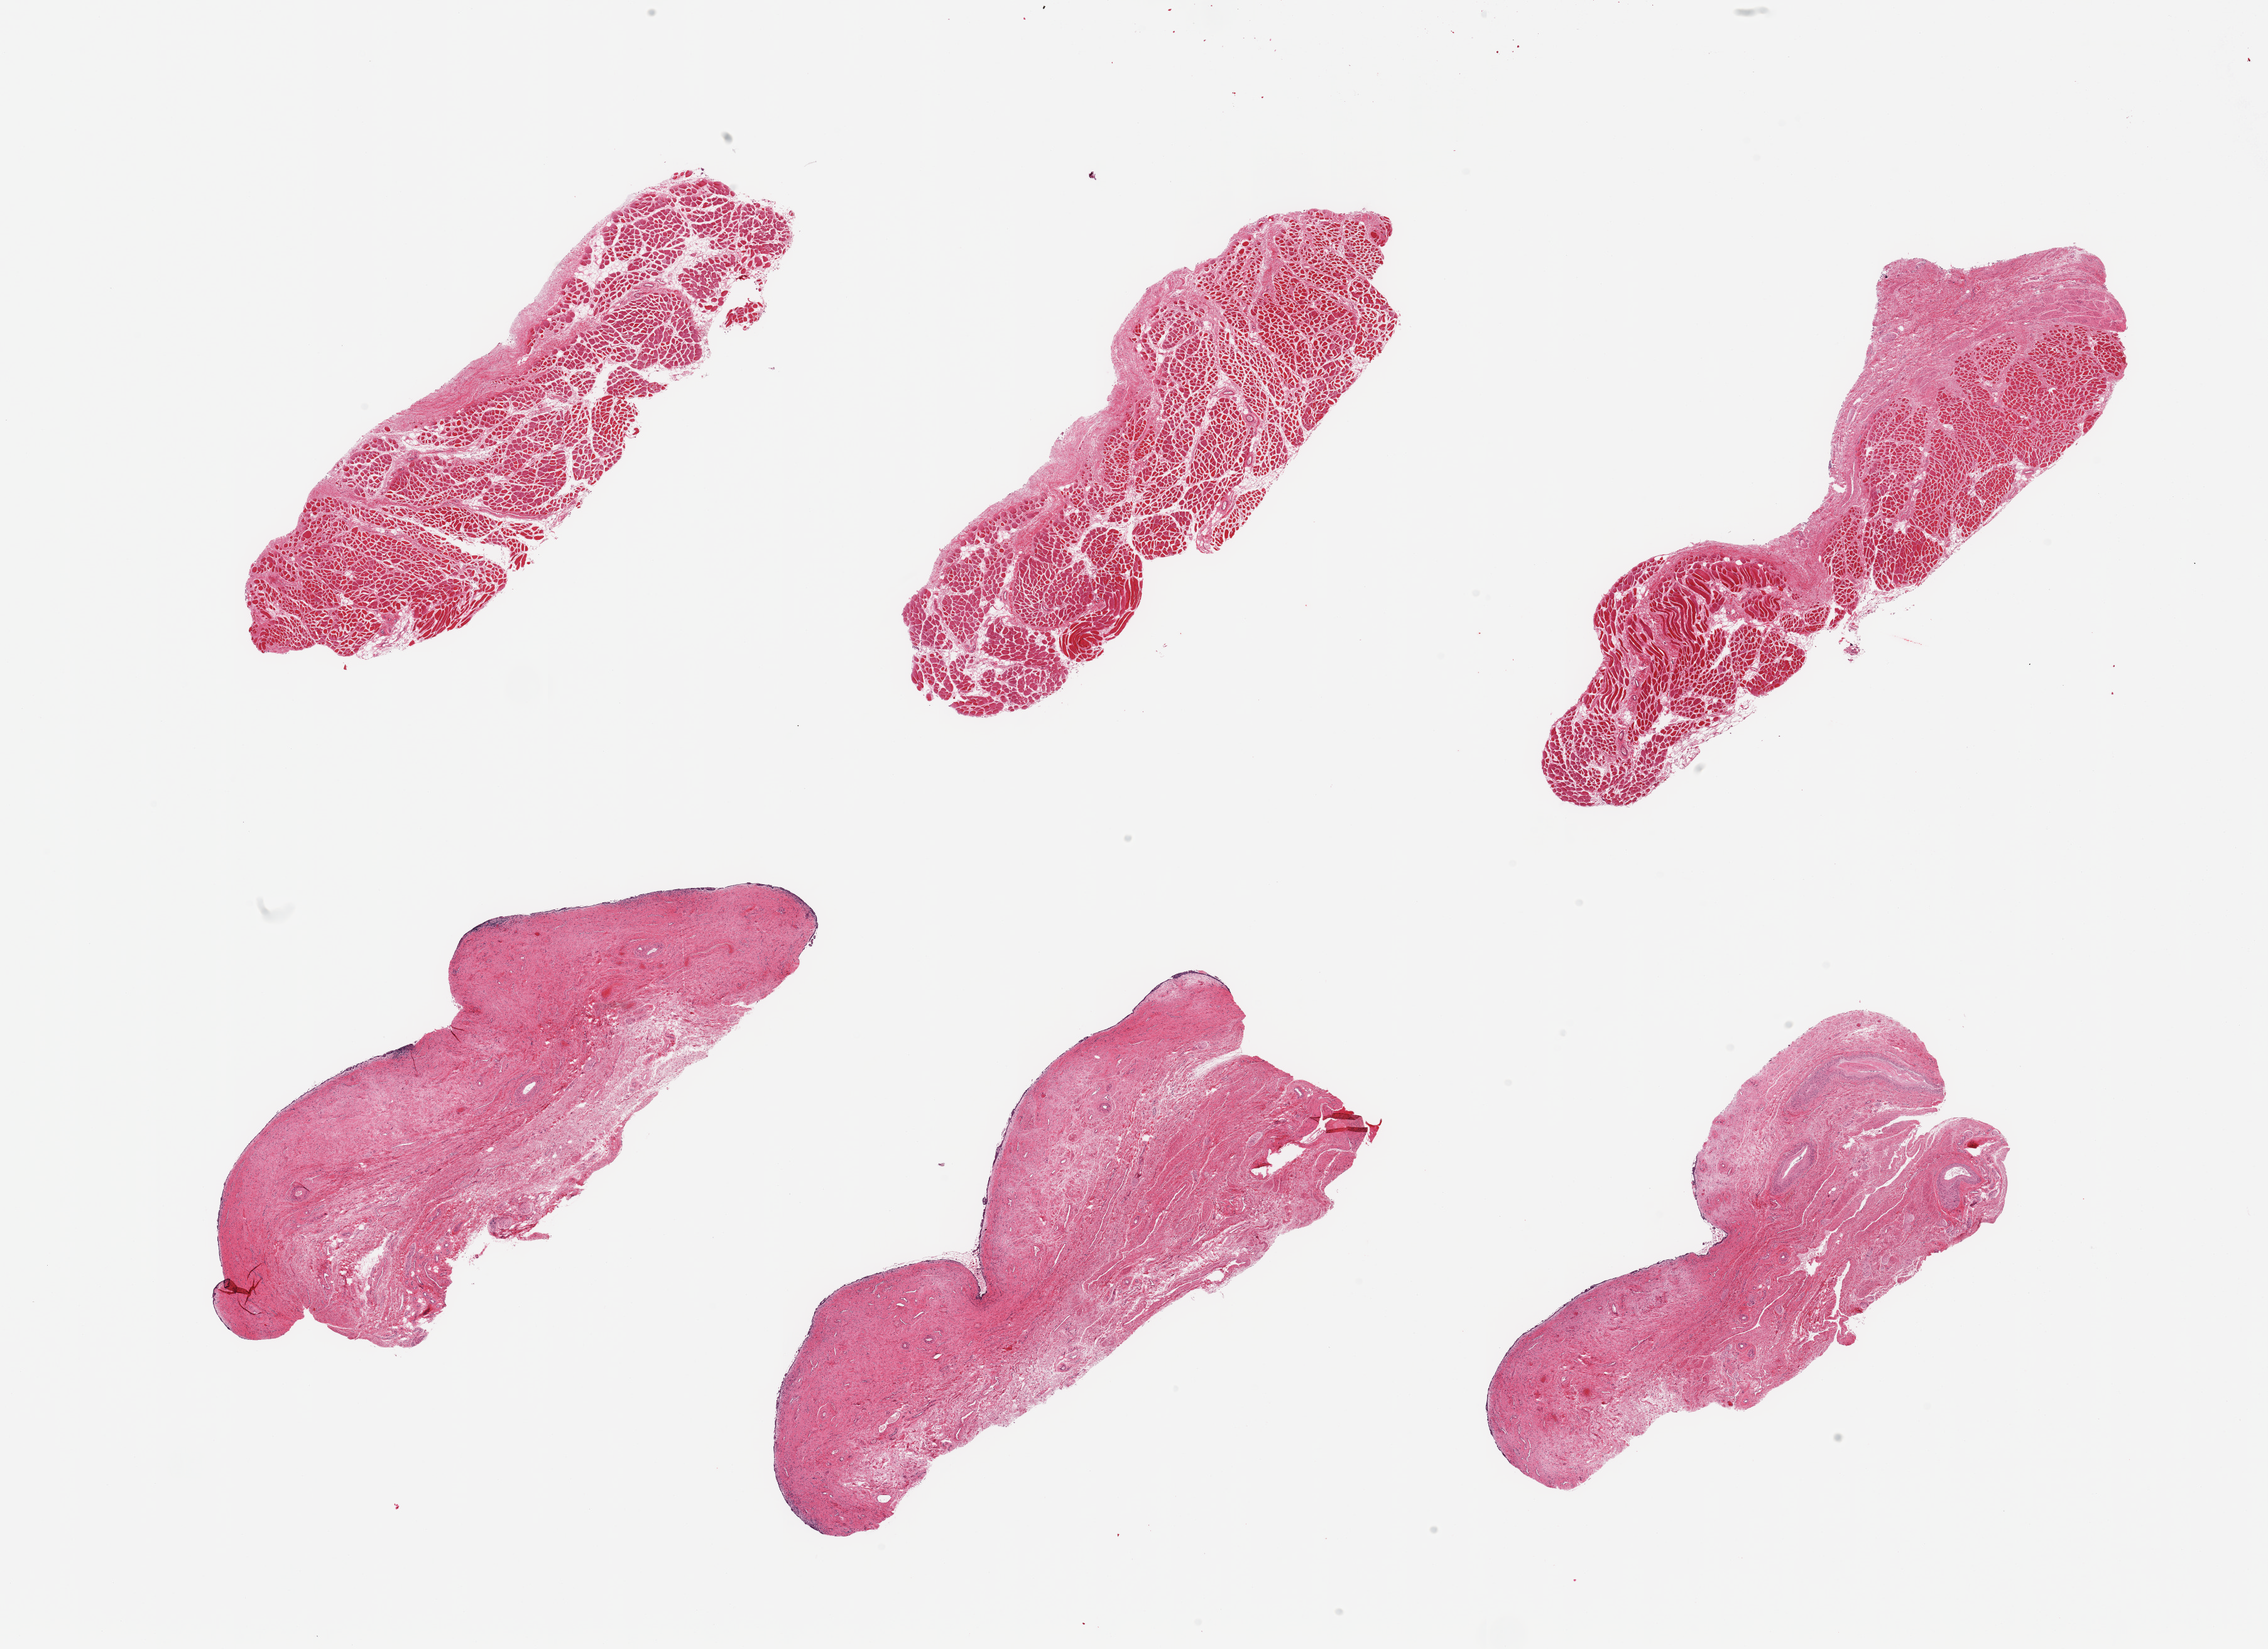
Digitized hematoxylin and eosin (H&E)-stained section, brightfield — low-resolution overview of the scanned area, about 28.5 x 20.8 mm, PAXgene-fixed paraffin-embedded (PFPE) section, sampled site (target tissue): vagina, donor tissue sample. Donor sex: female.
Reviewer comment on this tissue sample: 6 pieces; 3 cuts are vaginal wall with largely sloughed epithelium; 3 cuts (1 aliquot) are skeletal muscle.